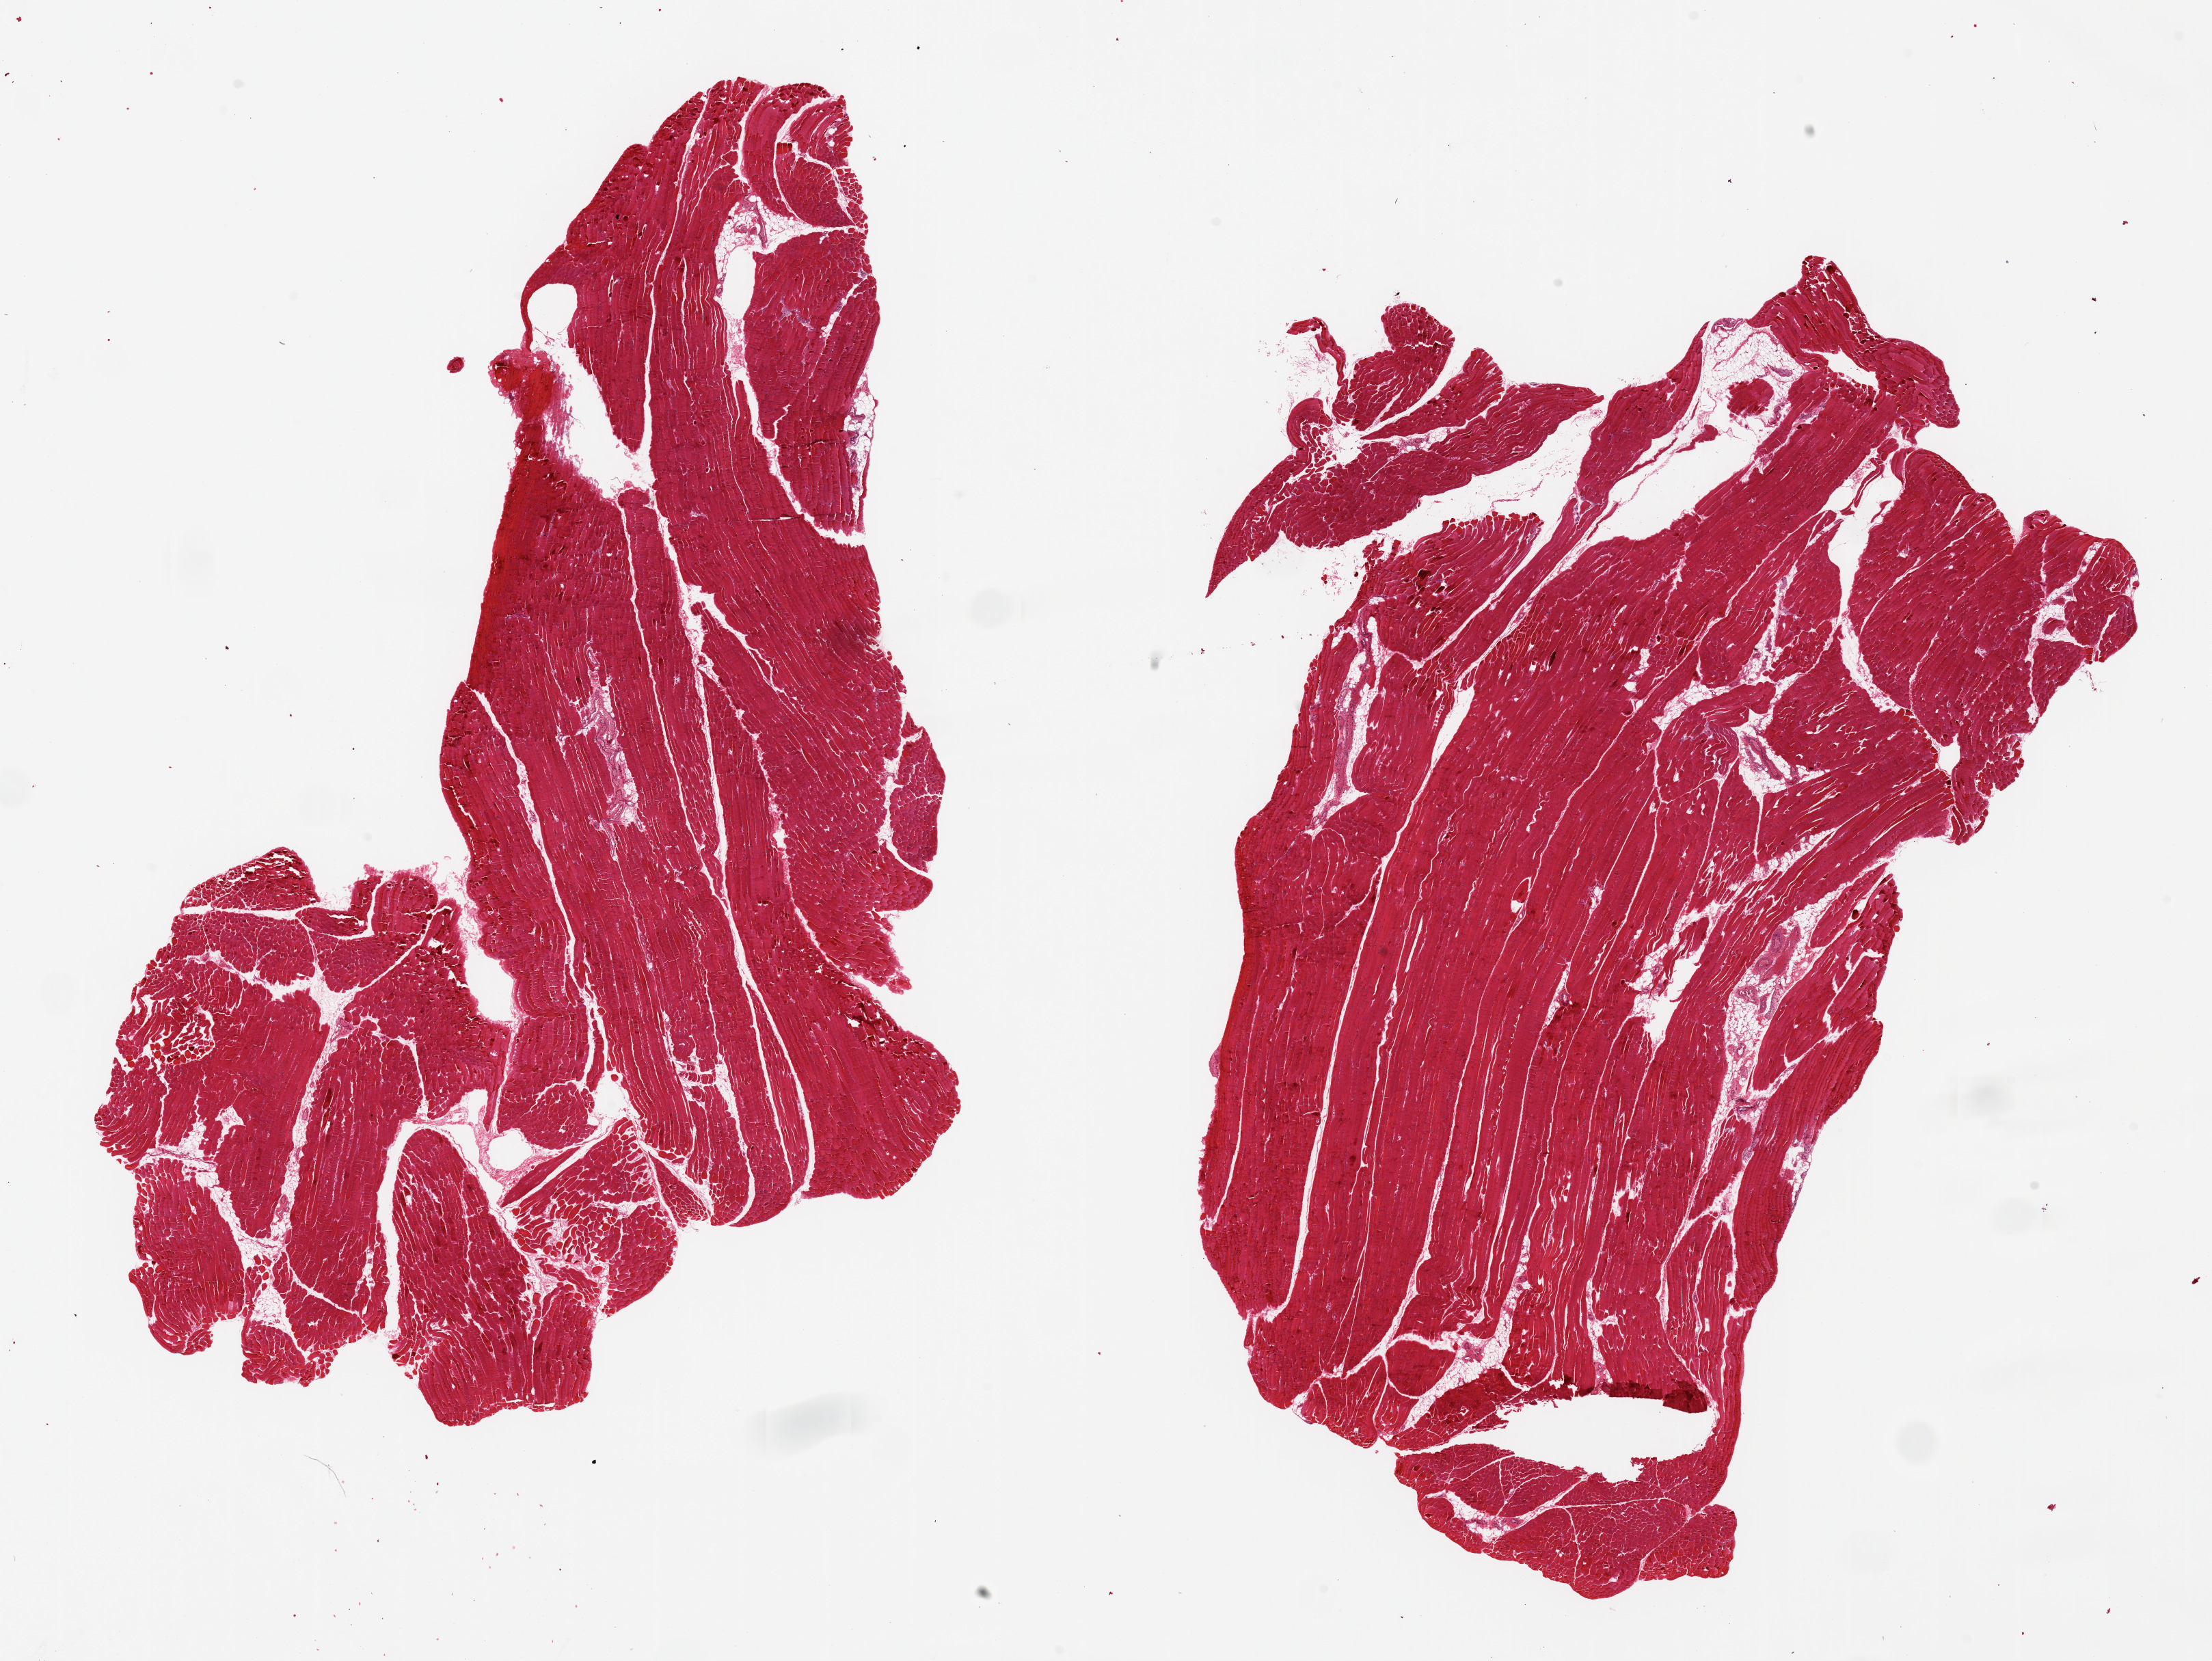
Digitized haematoxylin and eosin-stained section, brightfield — whole scanned area (about 25.6 x 19.2 mm) shown as a low-resolution overview. PAXgene-fixed, paraffin-embedded tissue. Sampled site (target tissue): skeletal muscle. Donor tissue sample. Donor: male.
• reviewer comment on this tissue sample: 2 pieces ~14x8mm. minimal interstitial fat